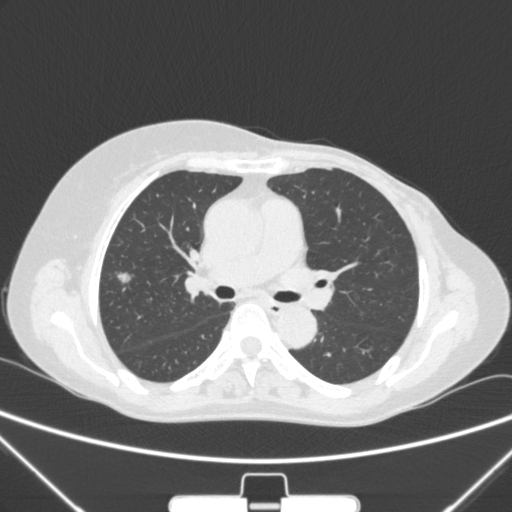
Chest CT, one axial slice; position 152 of 265 along the scan axis; 120 kVp; lung window (W 1500 / L -600 HU); 1 mm slice thickness; 512 × 512 image matrix. Female patient, age 64 years. From the clinical record (not read from this slice): clinical TNM (as recorded): T1c N0 M0; histopathological grade: G1-2.
Annotated regions visible in this slice (bounding box drawn by a radiologist):
- lung tumour (recorded histology: adenocarcinoma): bounding box (x1, y1, x2, y2) in pixels: (110, 257, 137, 292)